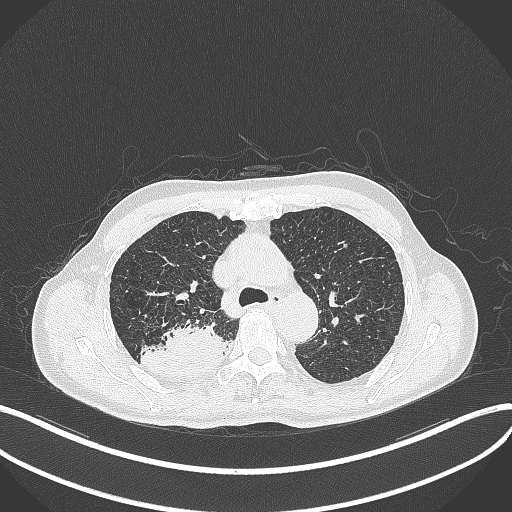
Chest CT, one axial slice. Slice 319 of 428 in the series (ordered by position). 120 kVp. Lung window (W 1500 / L -600 HU). 1 mm slice thickness. 512 × 512 image matrix, field of view 400 × 400 mm. Patient: male, 79 years. Case-level facts recorded for this patient, not image findings: clinical TNM (as recorded): T3 N0 M0.
Structures marked on this image (bounding box drawn by a radiologist):
- lung tumour (recorded histology: adenocarcinoma): bounding box (x1, y1, x2, y2) in pixels: (138, 321, 228, 382)